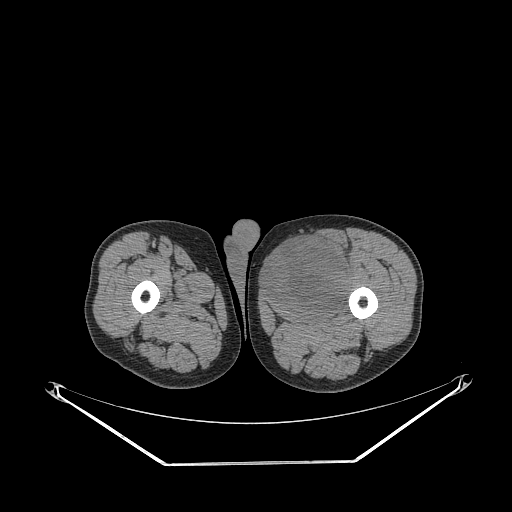
CT of an extremity soft-tissue mass (from a PET/CT study), one axial slice. Slice 252 of 267 in the series (ordered by position). Reconstruction kernel STANDARD. 140 kVp. Soft-tissue window (W 400 / L 40 HU). 512 × 512 image matrix, field of view 500 × 500 mm. Male patient. Case-level facts recorded for this patient, not image findings: histological type: pleiomorphic liposarcoma; grade: high; site of the primary tumour: left thigh.
Annotated regions visible in this slice (expert contour drawn on MRI and transferred to this co-registered scan by the dataset authors):
- gross tumour volume including surrounding oedema: box from (x=265, y=237) to (x=353, y=312) px
- gross tumour volume (mass): (x=265, y=237)–(x=350, y=312)